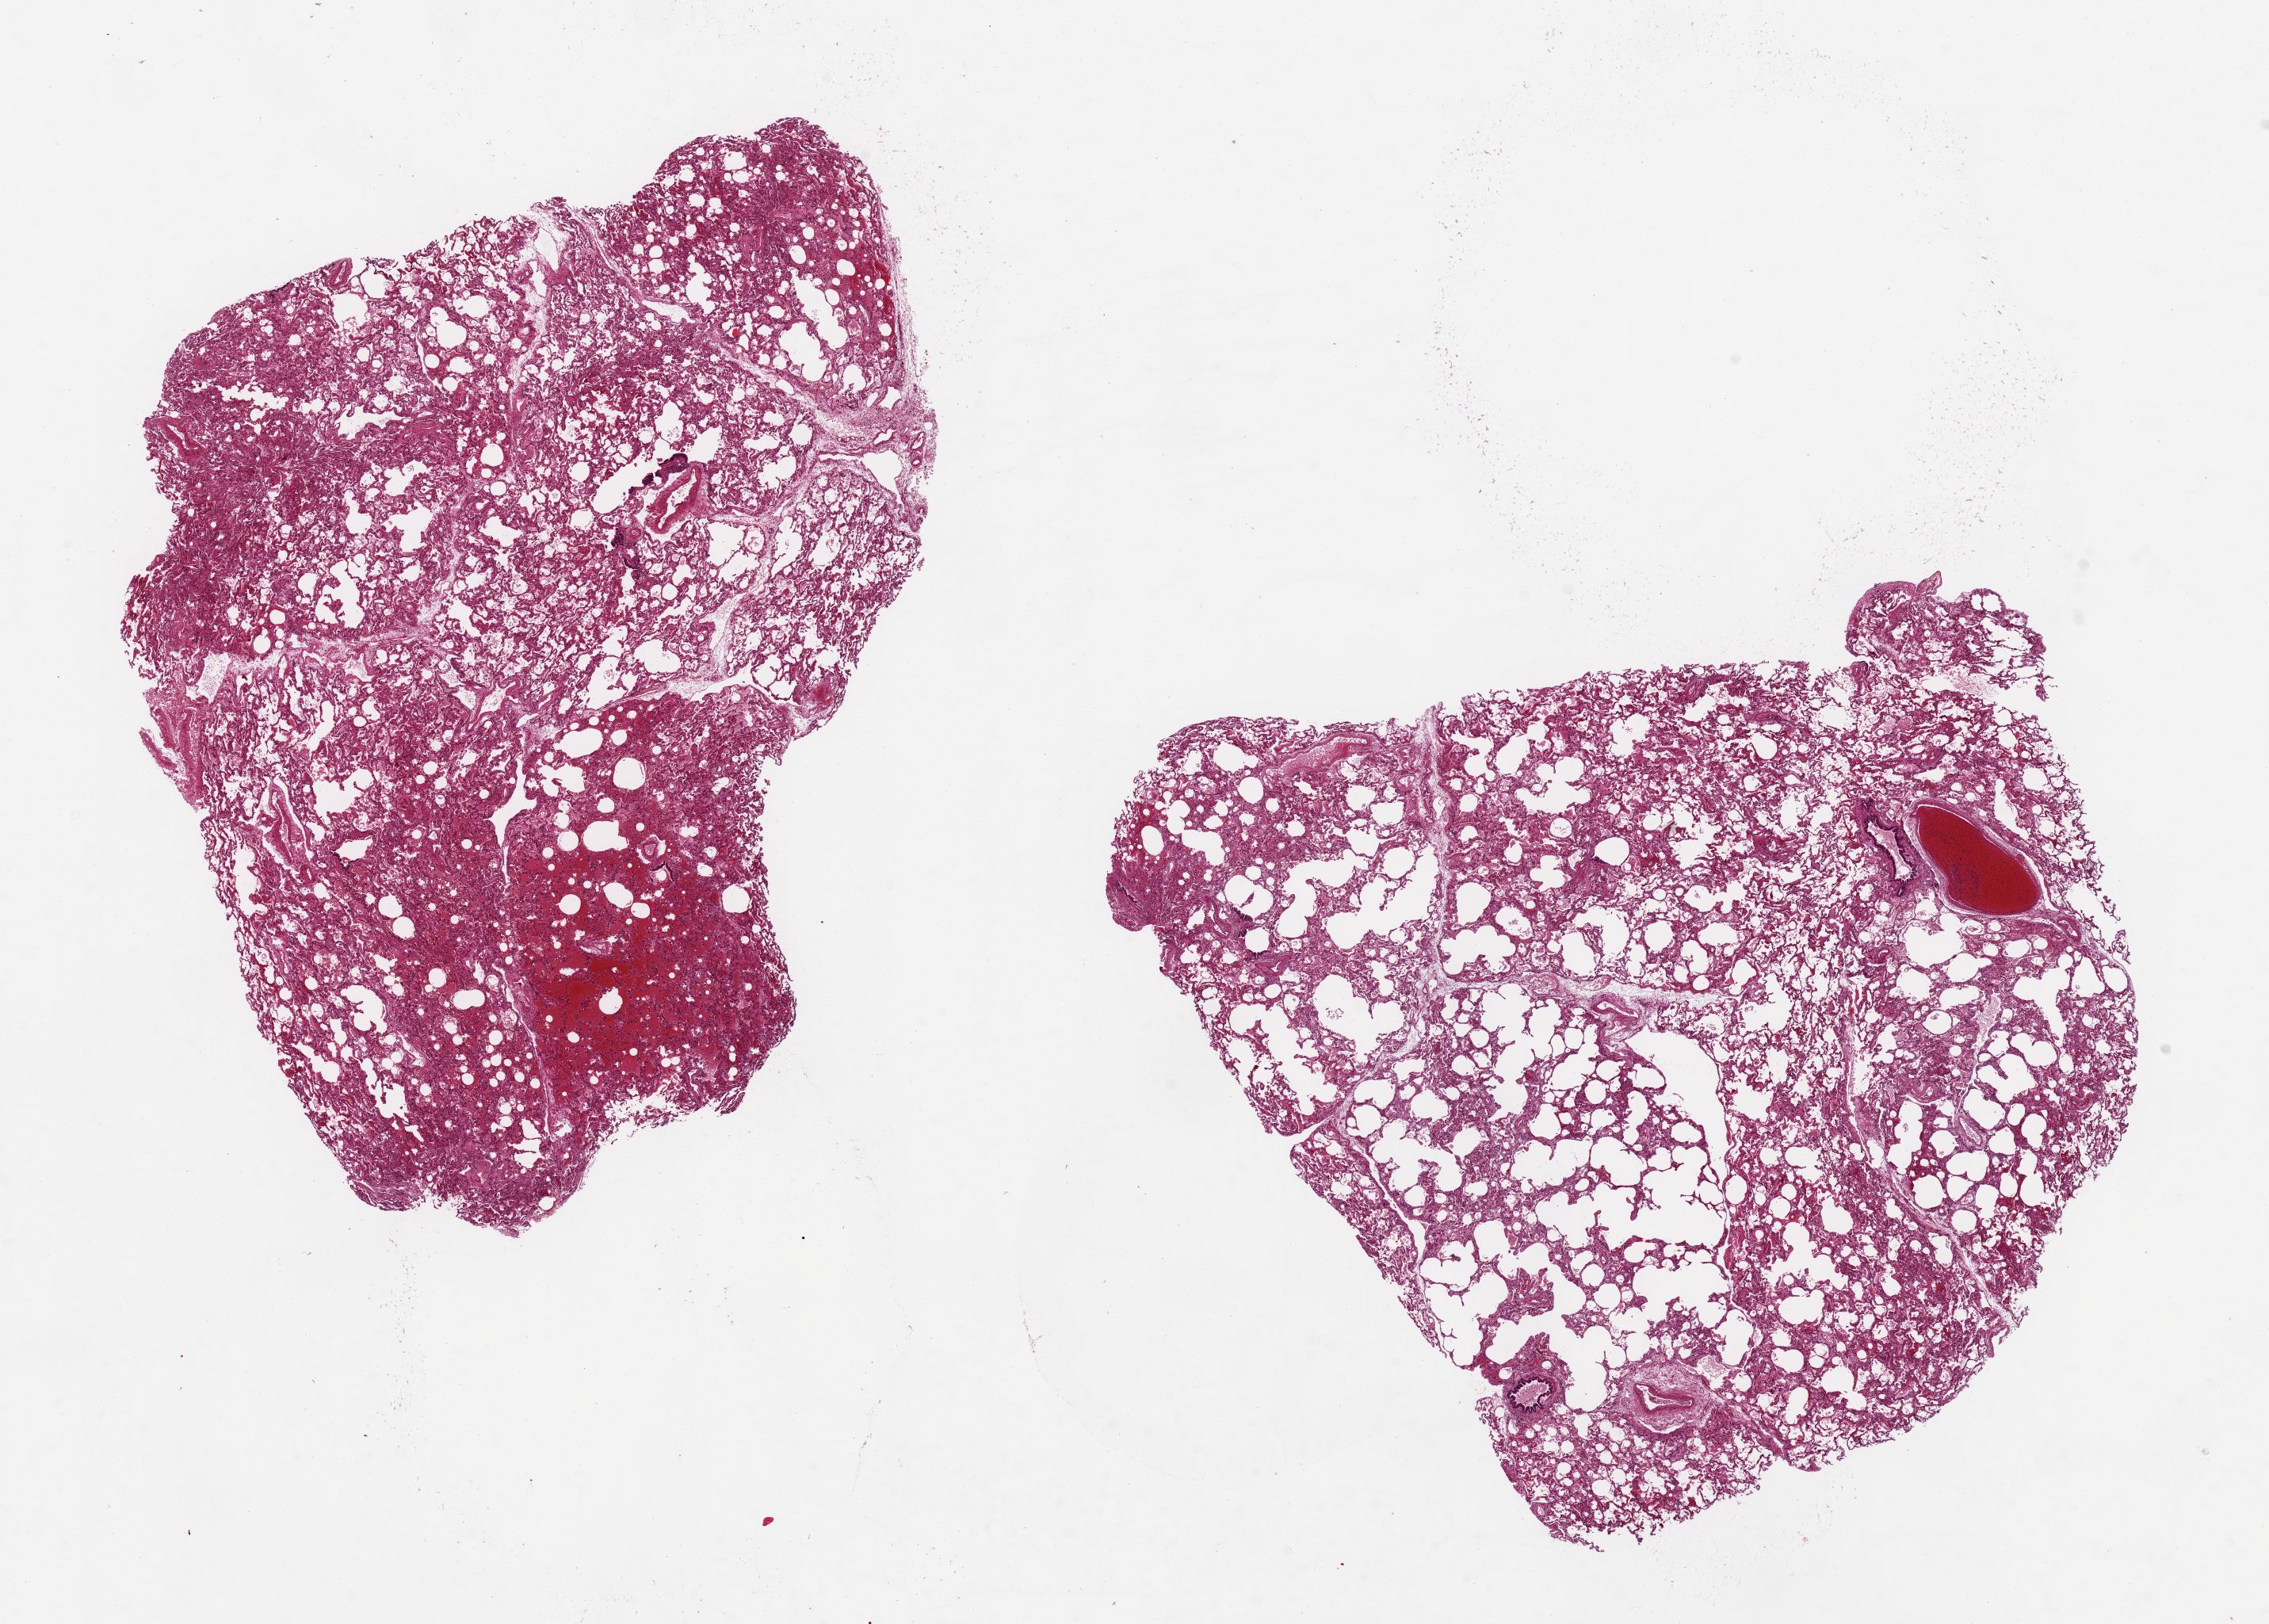
Whole-slide image, hematoxylin and eosin (H&E) stain, shown as a low-resolution overview of the whole scanned area (about 22.6 x 16.2 mm, from a 20x scan). PAXgene-fixed paraffin-embedded (PFPE) section. Sampled site (target tissue): lung. Donor tissue sample. Donor: female.
- pathologist's review note for this sample: 2 aliquots ~9x8mm. Patchy marked congestion/hemorrhage